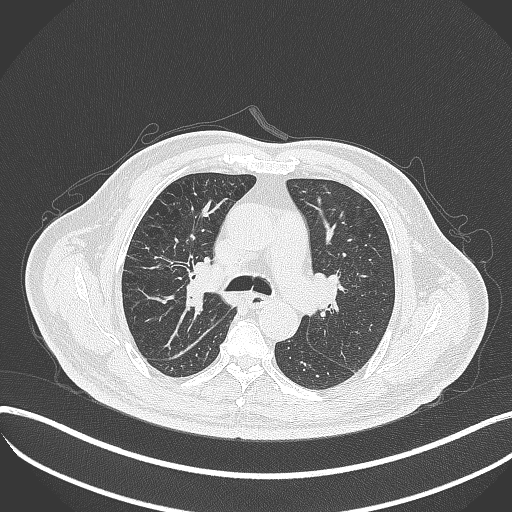
Chest CT, one axial slice. Position 236 of 401 along the scan axis. Reconstruction kernel B70f. 120 kVp. Lung window (W 1500 / L -600 HU). 1 mm slice thickness. 512 × 512 image matrix, field of view 400 × 400 mm. Male patient, age 72 years. Case-level facts recorded for this patient, not image findings: clinical TNM (as recorded): T1c N0 M0.
Outlined on this slice (bounding box drawn by a radiologist):
- lung tumour (recorded histology: squamous cell carcinoma): bounding box [x1, y1, x2, y2] px = [173, 261, 208, 316]